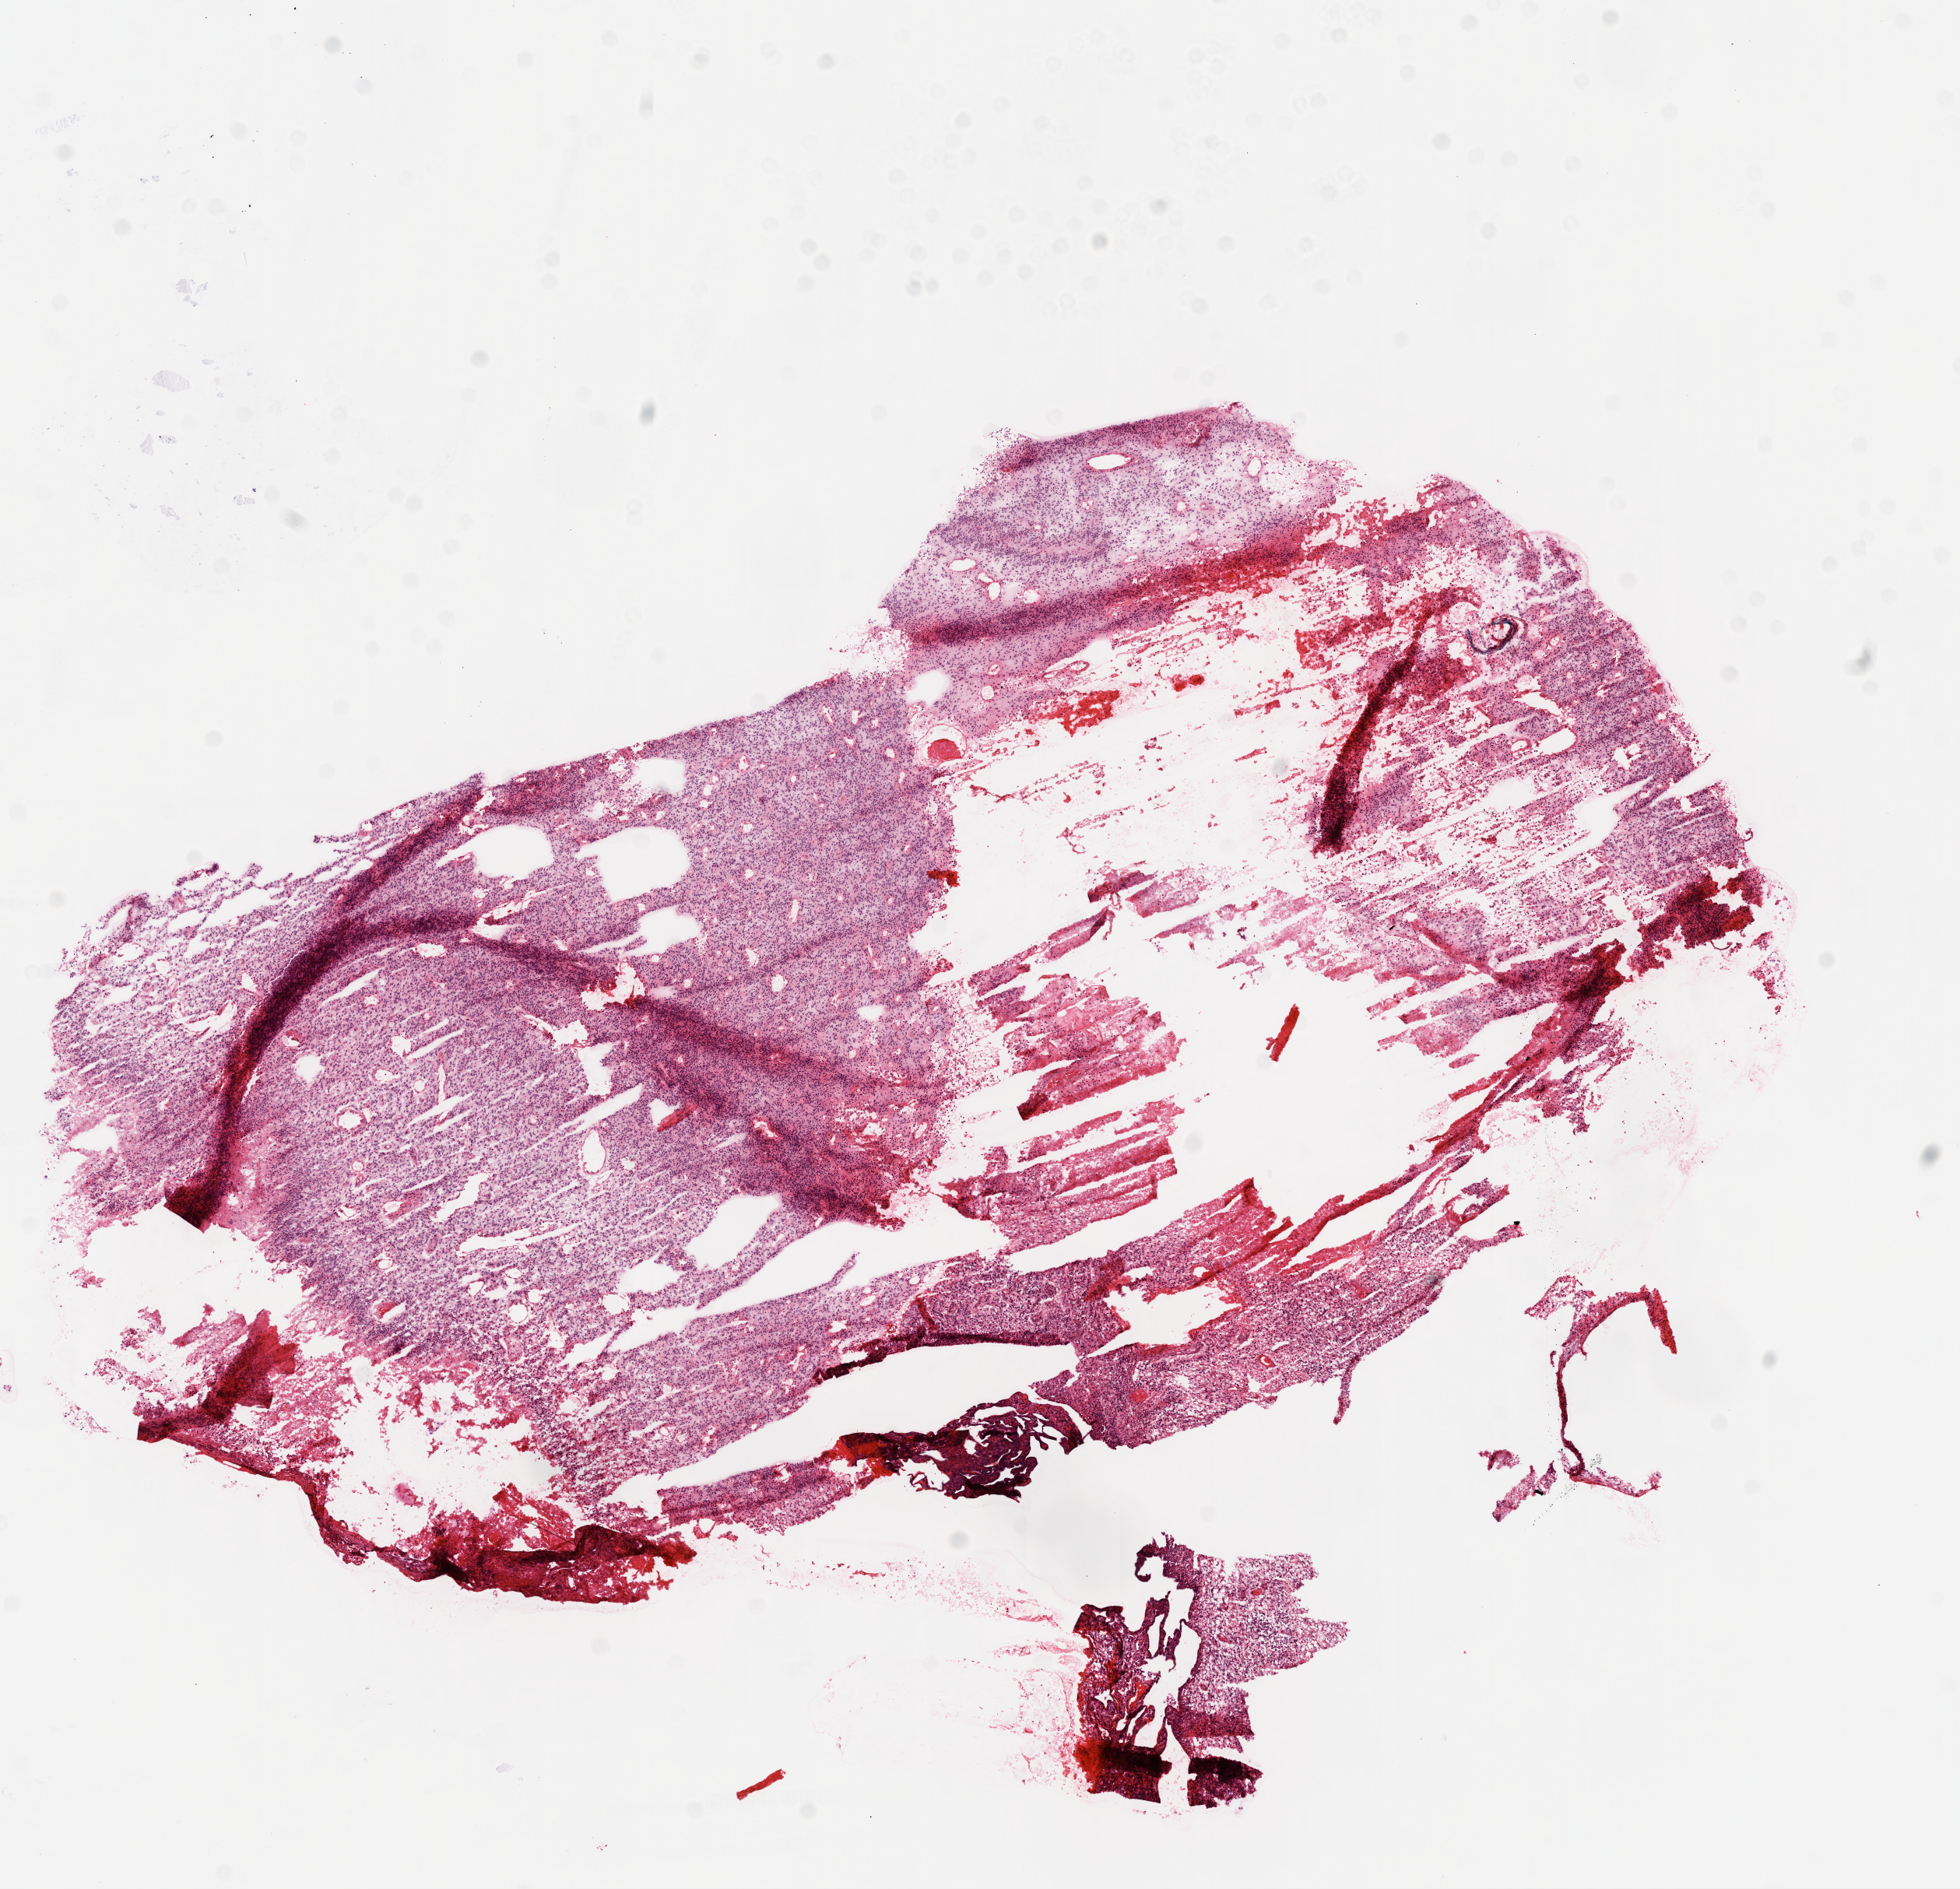
Whole-slide histology image, H&E-stained — low-resolution overview of the scanned area, about 10.2 x 9.8 mm, frozen section from the bottom of the tissue portion, primary tumour sample from the brain. Male, age 50 years at initial diagnosis. Slide review estimates, as recorded: tumour cells 80%, tumour nuclei 95%, normal cells 0%, stromal cells 5%, necrosis 15%.
Histologic diagnosis: Glioblastoma.